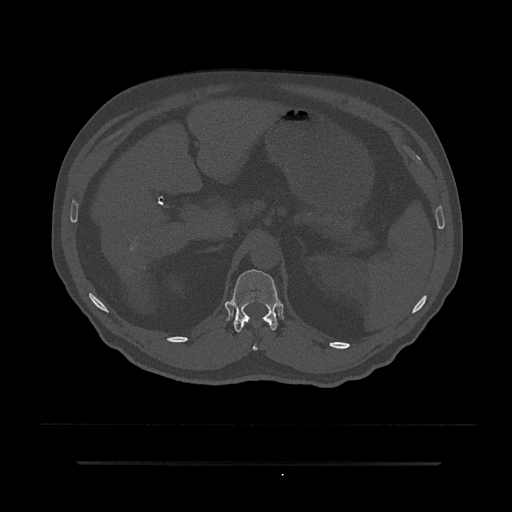
CT including the spine, one axial slice. Slice 219 of 797 in the series (ordered by position). Reconstruction kernel Br40s/3. 120 kVp. Bone window (W 1800 / L 400 HU). 0.5 mm slice thickness. 512 × 512 image matrix. Male patient, age 59 years. From the clinical record (not read from this slice): primary cancer: bile ducts.
Outlined on this slice (semi-automatic segmentation, software-assisted and operator-edited):
- T12 vertebra: box from (x=228, y=269) to (x=280, y=351) px